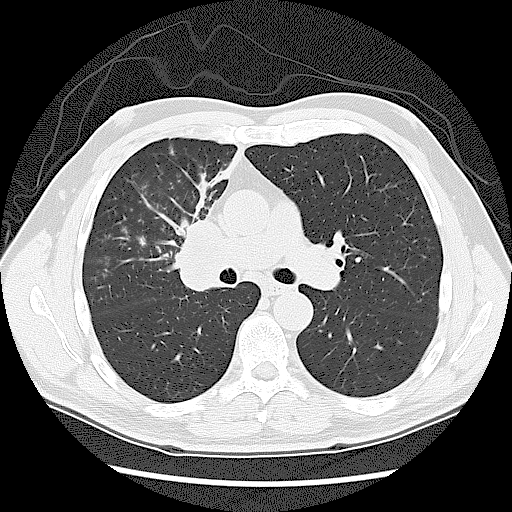
Low-dose screening chest CT, axial slice; baseline screening round; lung window (W 1500 / L -600 HU); 120 kVp; 512 × 512 image matrix. Male participant, aged 60 years at enrolment.
Lesion marked by an expert reader, bounding box (x1, y1, x2, y2) in pixels: (158, 218, 241, 310). No non-calcified nodule or mass ≥4 mm was recorded by the screening reader at this exam. Official screen result: negative screen, significant abnormalities not suspicious for lung cancer. Later outcome: lung cancer diagnosed 41 days after this screen — small cell carcinoma, NOS, right upper lobe, stage IIIA (AJCC 6th edition).